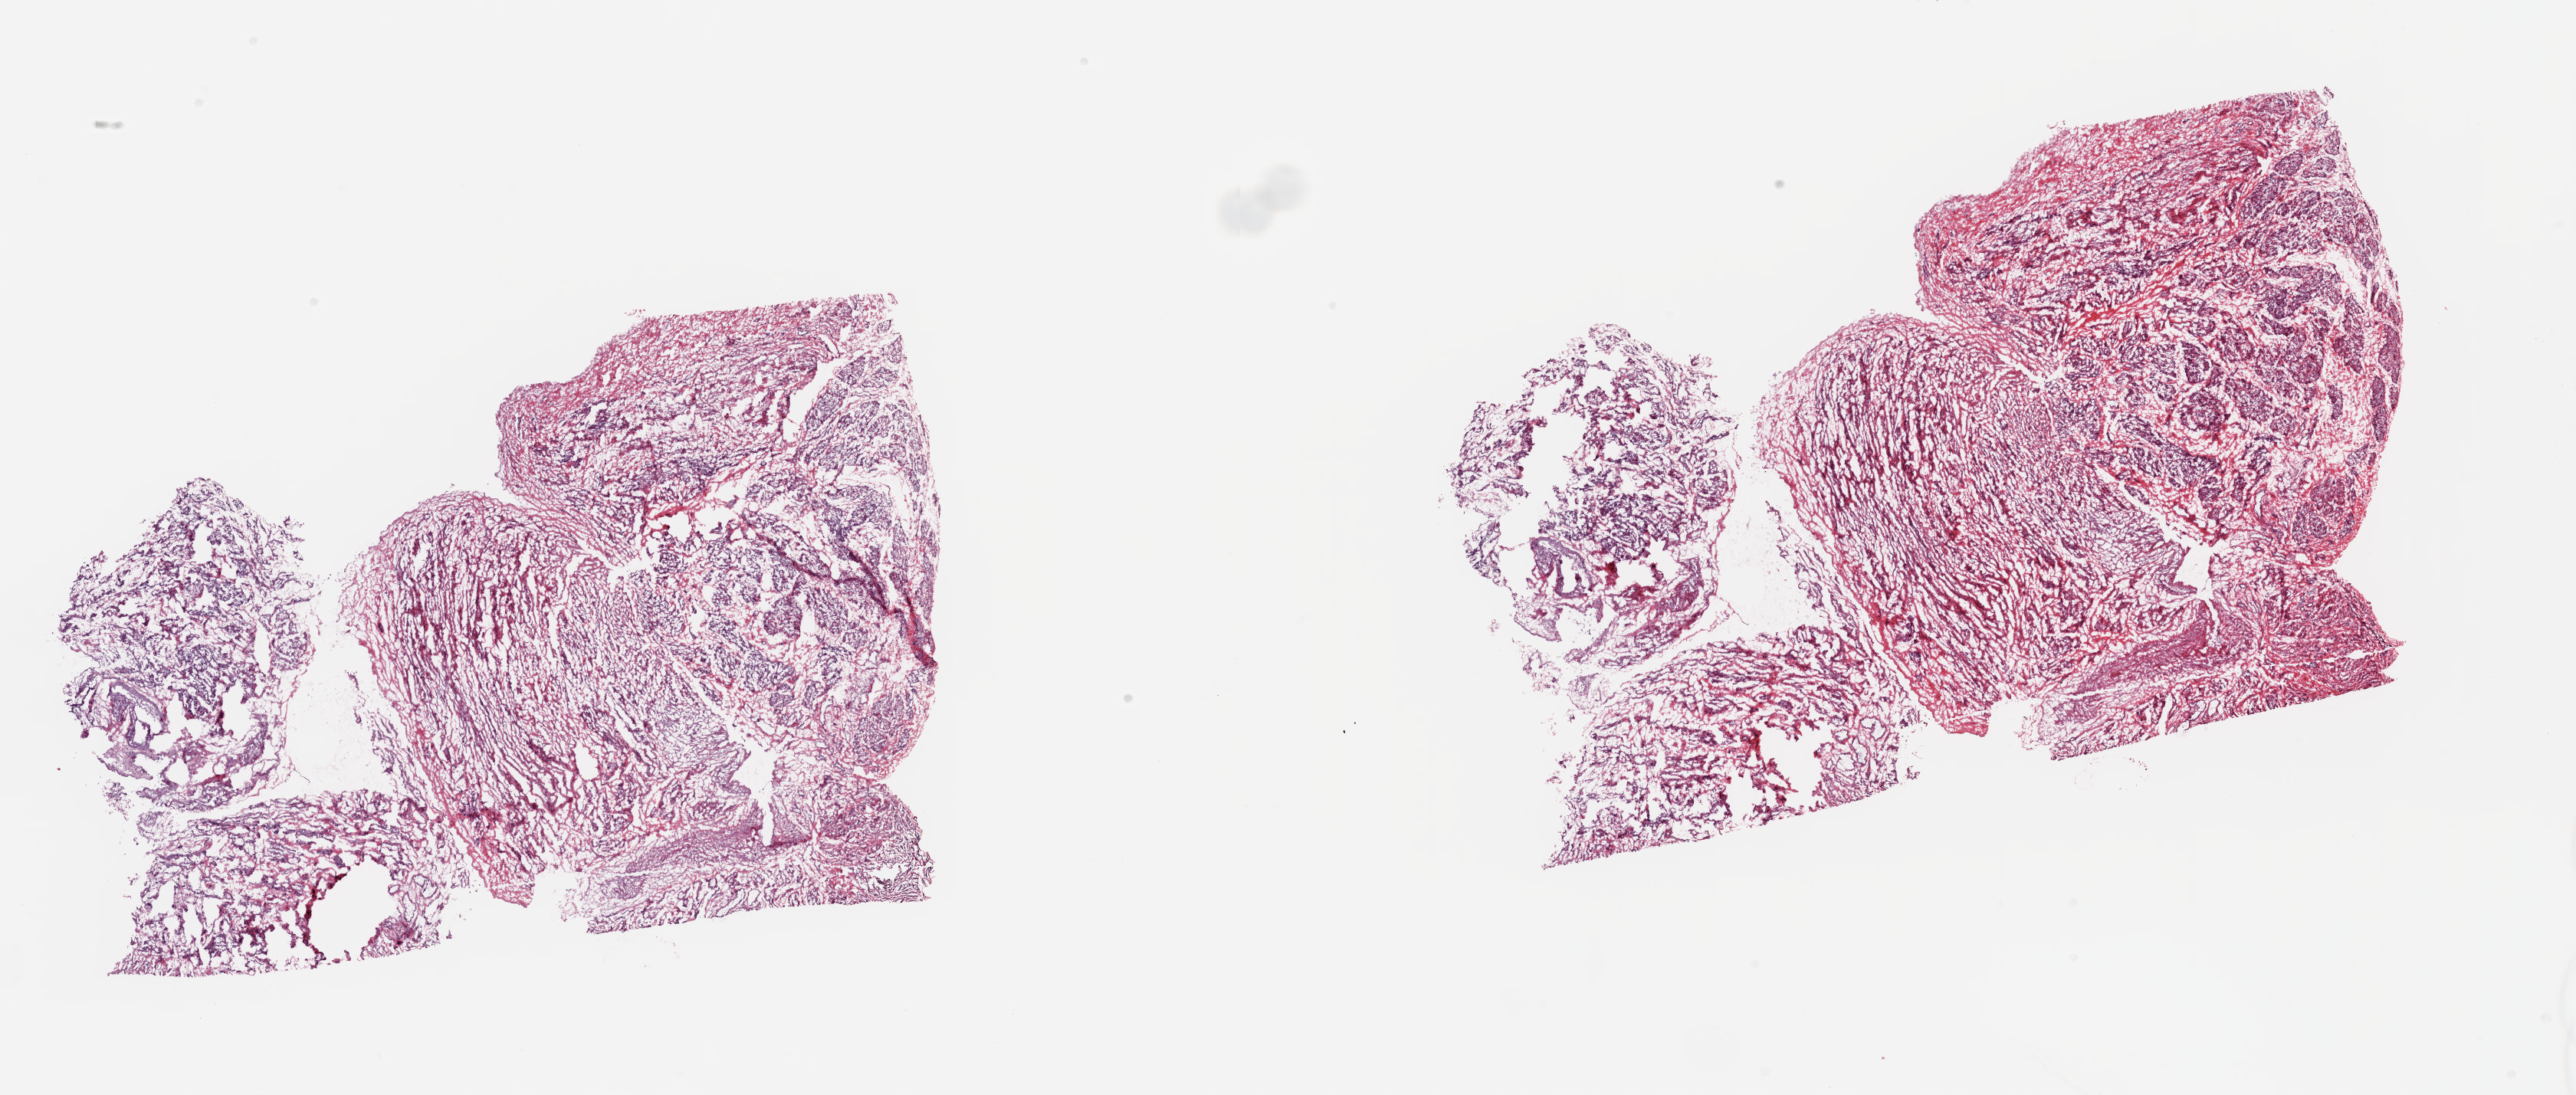
Whole-slide histology image, H&E — low-resolution overview of the scanned area, about 26.6 x 11.3 mm; frozen section from the top of the tissue portion; uterus, solid tissue normal (non-tumour tissue) sample. Female, age 66 years at initial diagnosis. Slide review estimates, as recorded: tumour cells 0%, tumour nuclei 0%, normal cells 100%, stromal cells 0%, necrosis 0%. Infiltration values recorded for this section: lymphocyte infiltration 0%, monocyte infiltration 0%, neutrophil infiltration 0%.
• this section: solid tissue normal sample (biorepository sample class)
• patient diagnosis: Serous cystadenocarcinoma, NOS (endometrium)